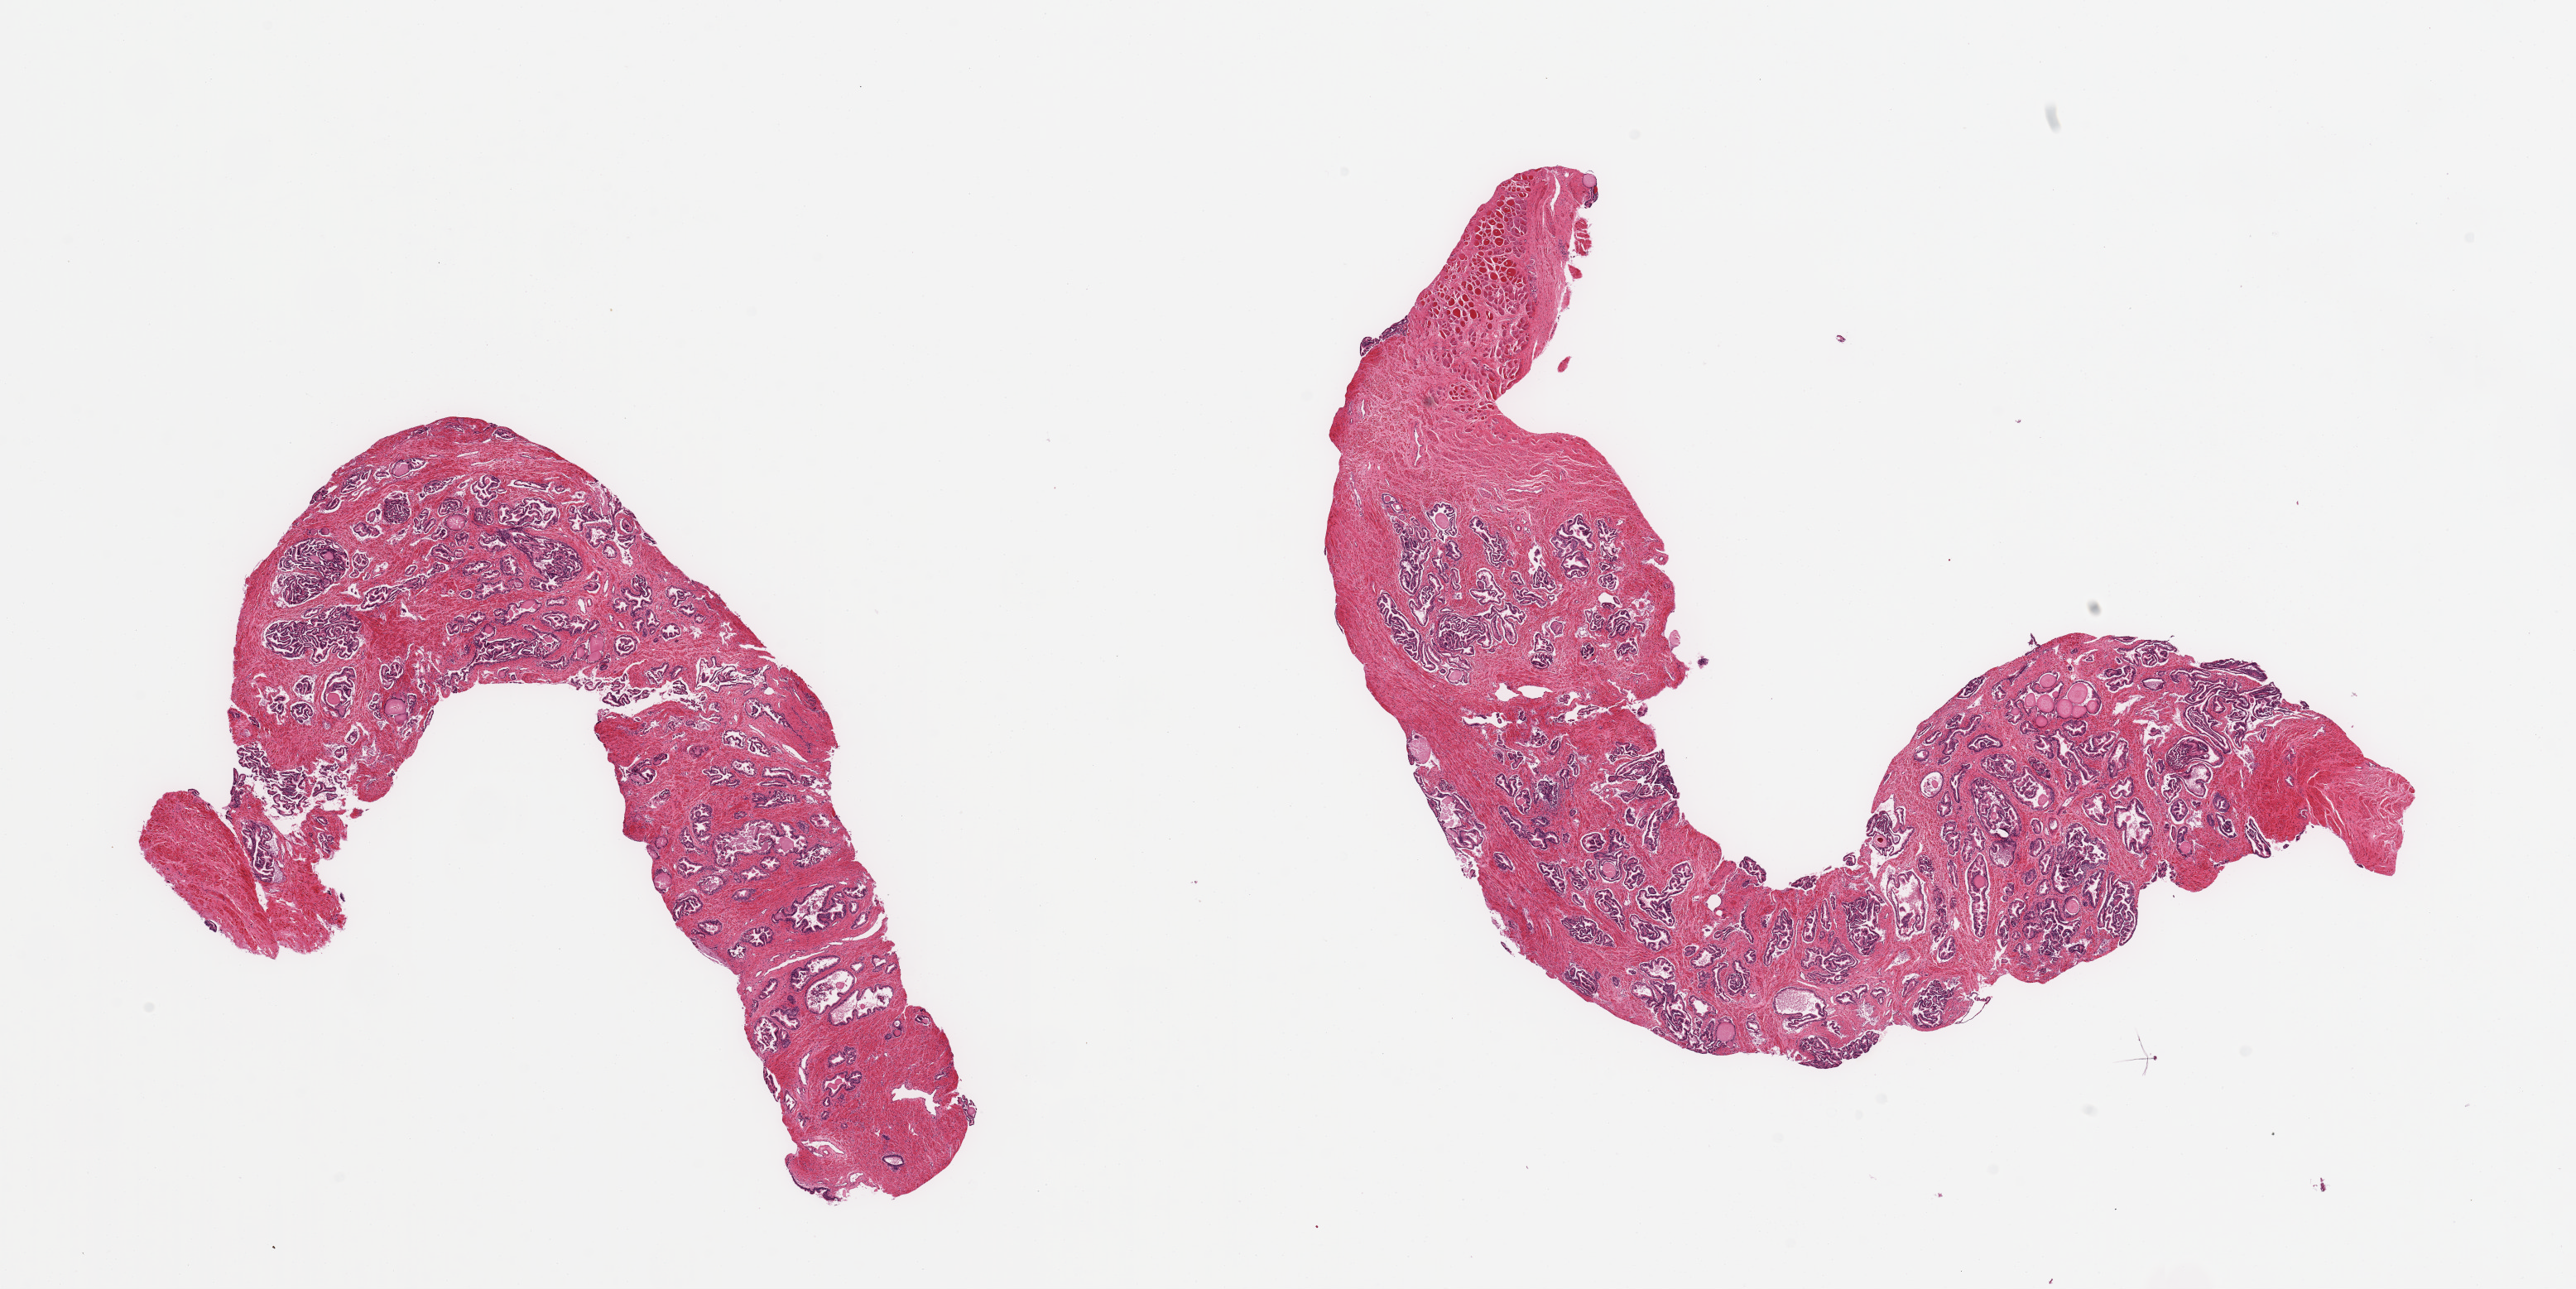
Digitized hematoxylin and eosin (H&E)-stained section, low-resolution overview of the scanned area, about 24.6 x 12.3 mm (from a 20x scan), PAXgene-fixed, paraffin-embedded tissue, section of prostate (target tissue), tissue donor sample.
Pathologist's review note for this sample: 2 pieces; fibromuscular stroma and glandular hyperplasia with amylaceous bodies.